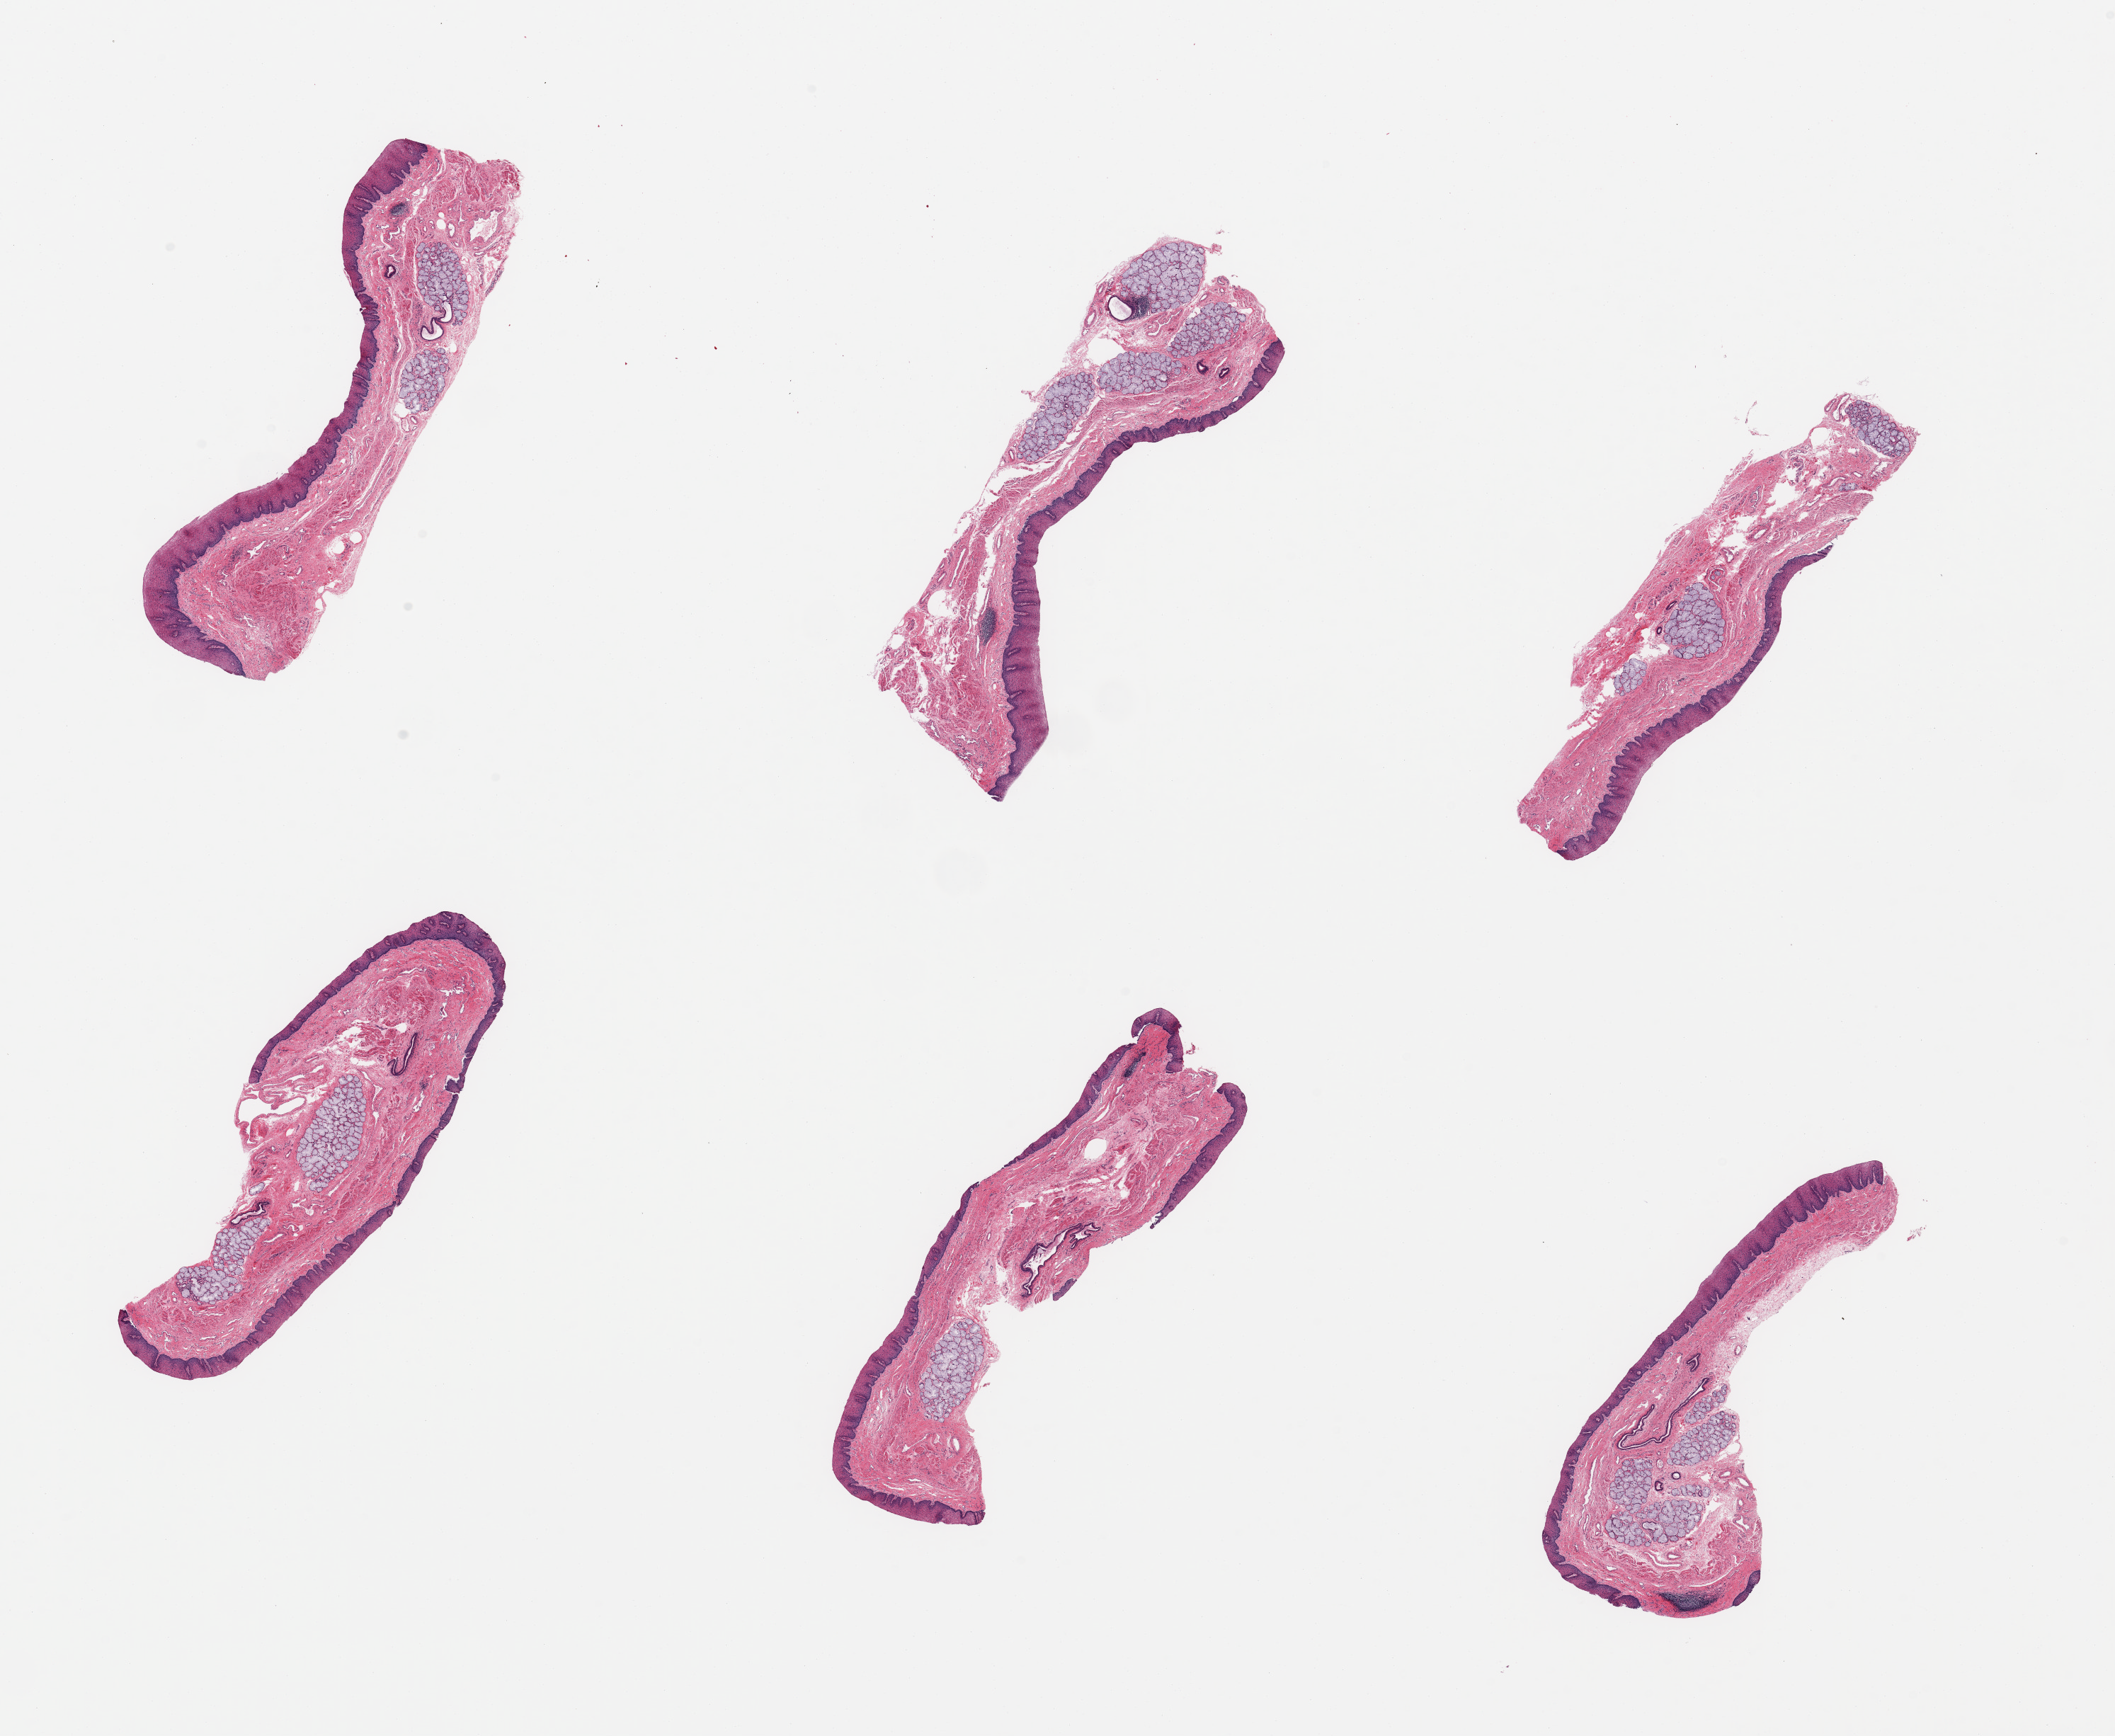
Whole-slide image, hematoxylin and eosin (H&E) stain, brightfield, a low-resolution overview of the entire scanned area, about 23.6 x 19.4 mm (slide scanned at 20x); PAXgene-fixed, paraffin-embedded tissue; sampled site (target tissue): esophageal mucous membrane; tissue donor sample. Donor sex: male.
Pathologist's review note for this sample: 6 pieces; ~0.4 mm thick squamous epithelium; many submucosal glands.